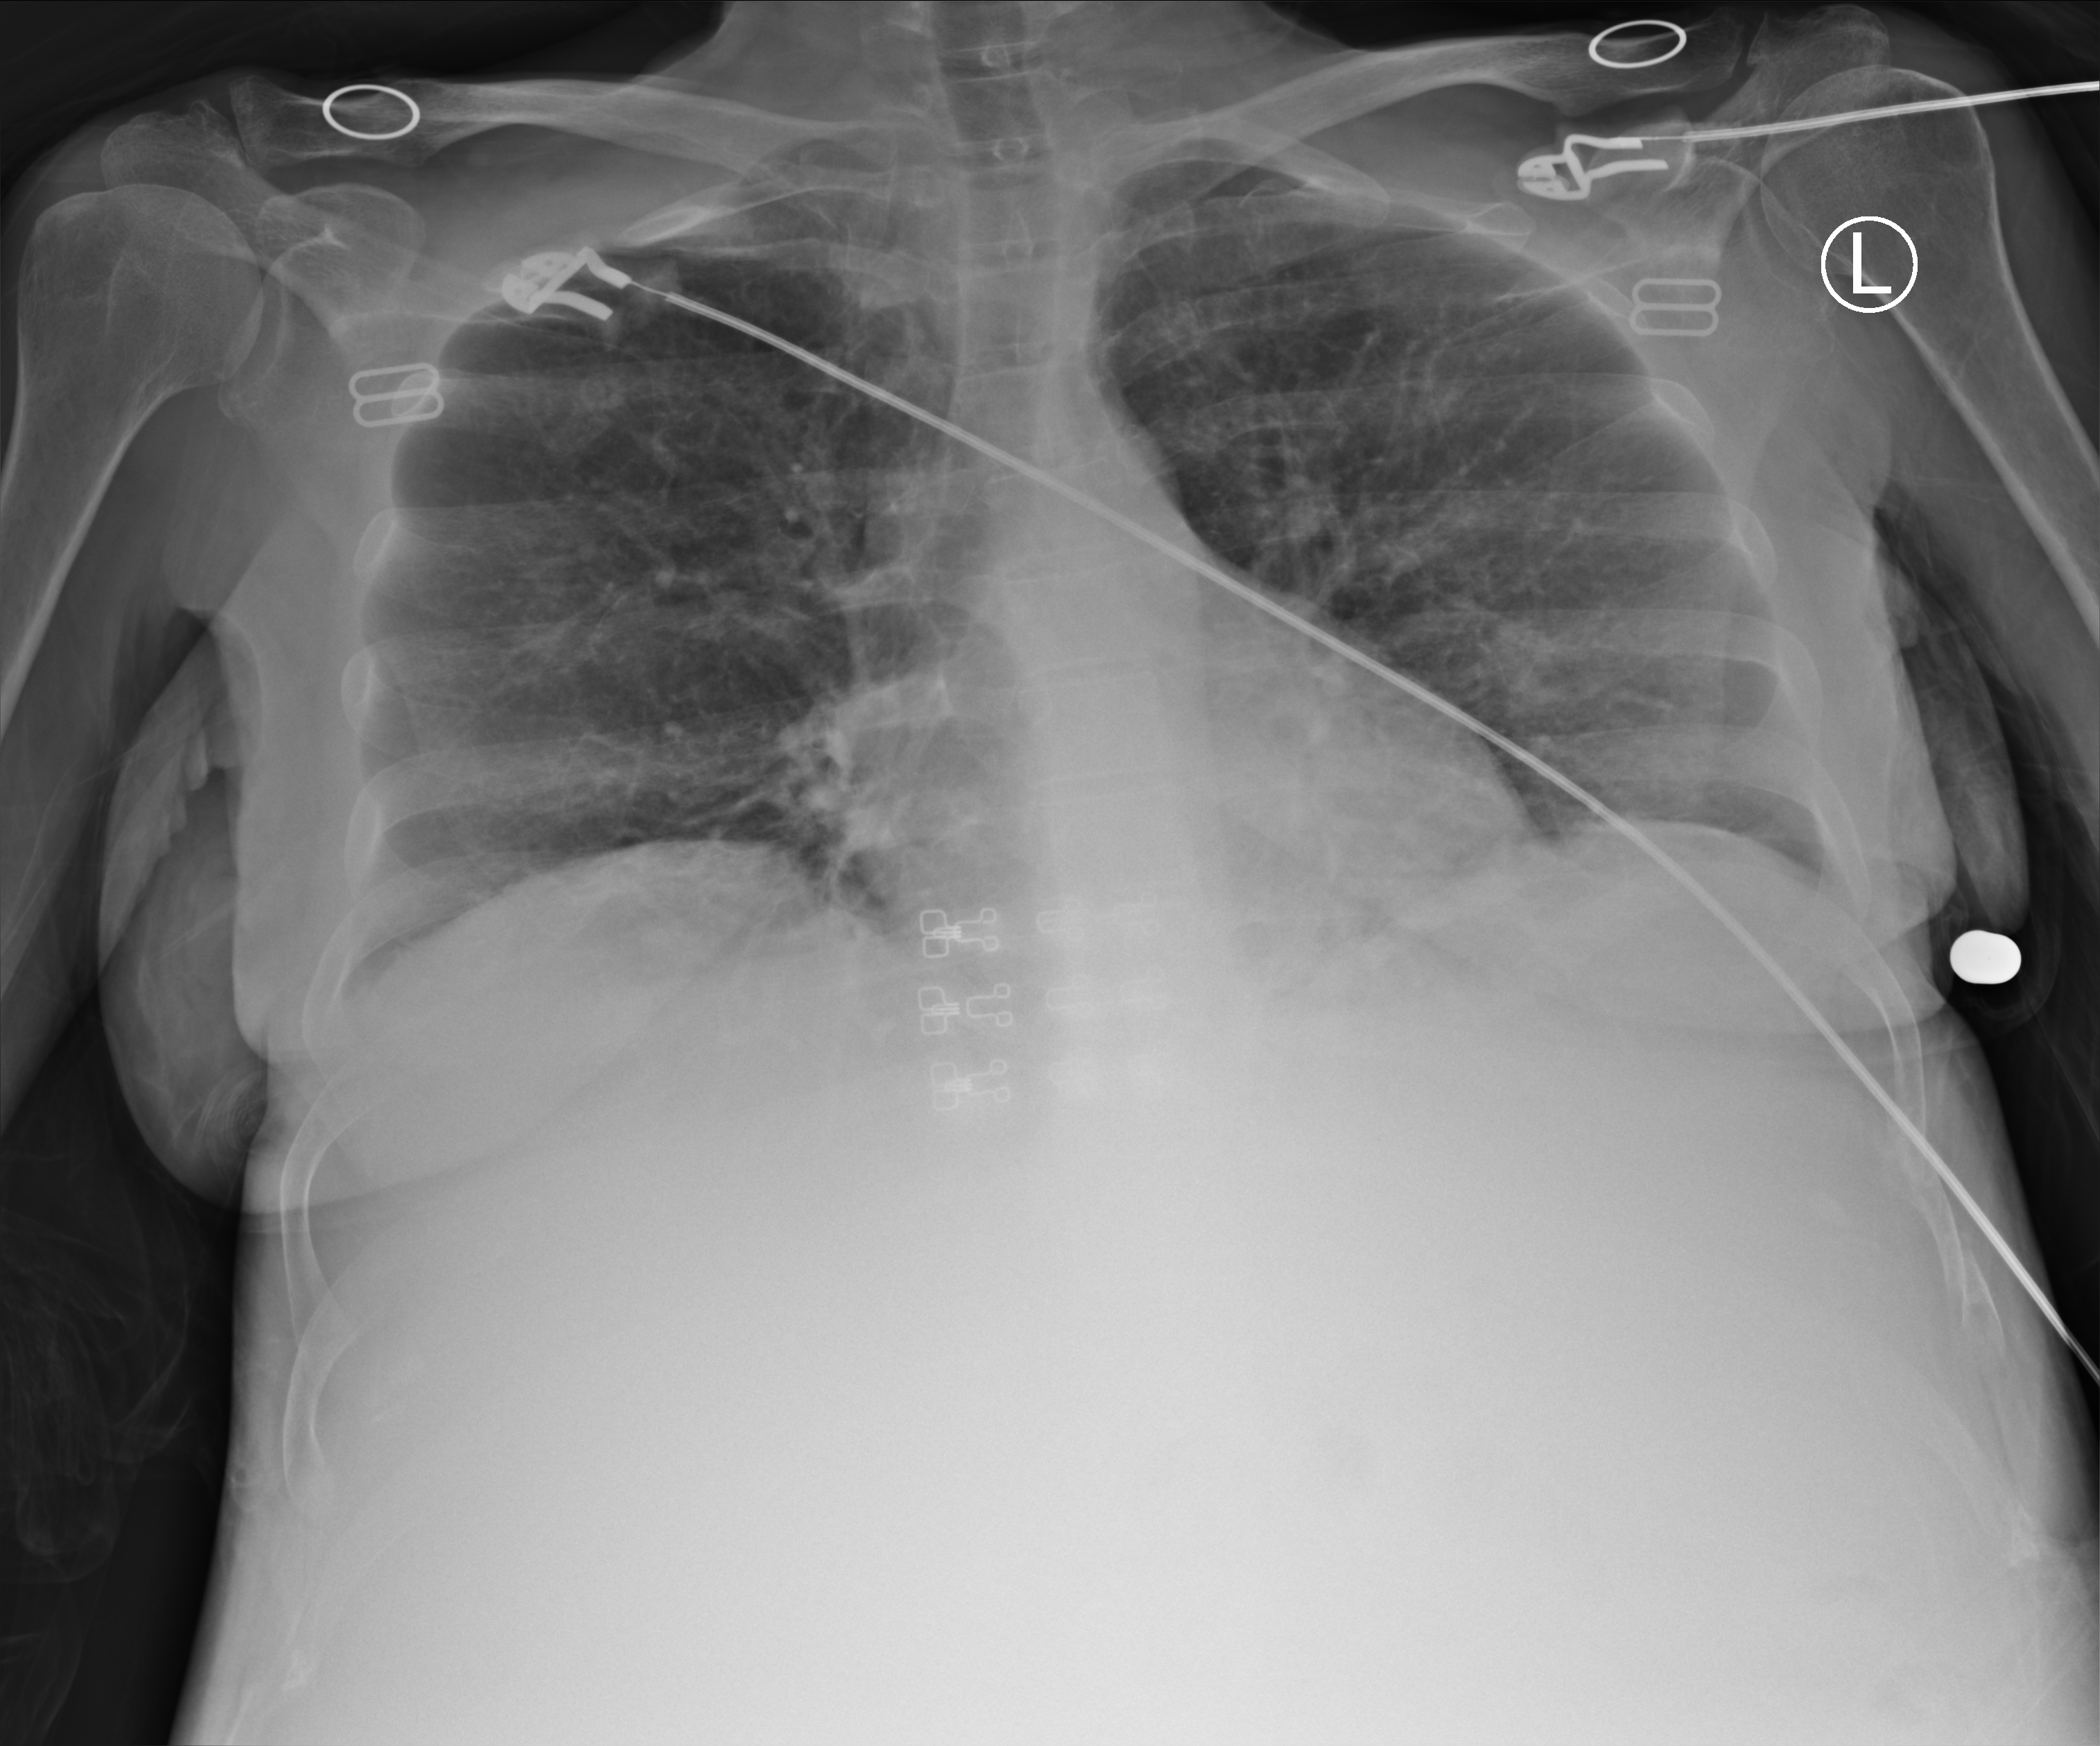
Bedside chest radiograph (computed radiography); anteroposterior (AP) projection. Female patient hospitalised with COVID-19, age 18–59 years.
Hospital-stay facts (about this admission, not read from this image; timing relative to this image not recorded):
- mechanically ventilated during this hospital stay: no
- length of hospital stay: 13 days